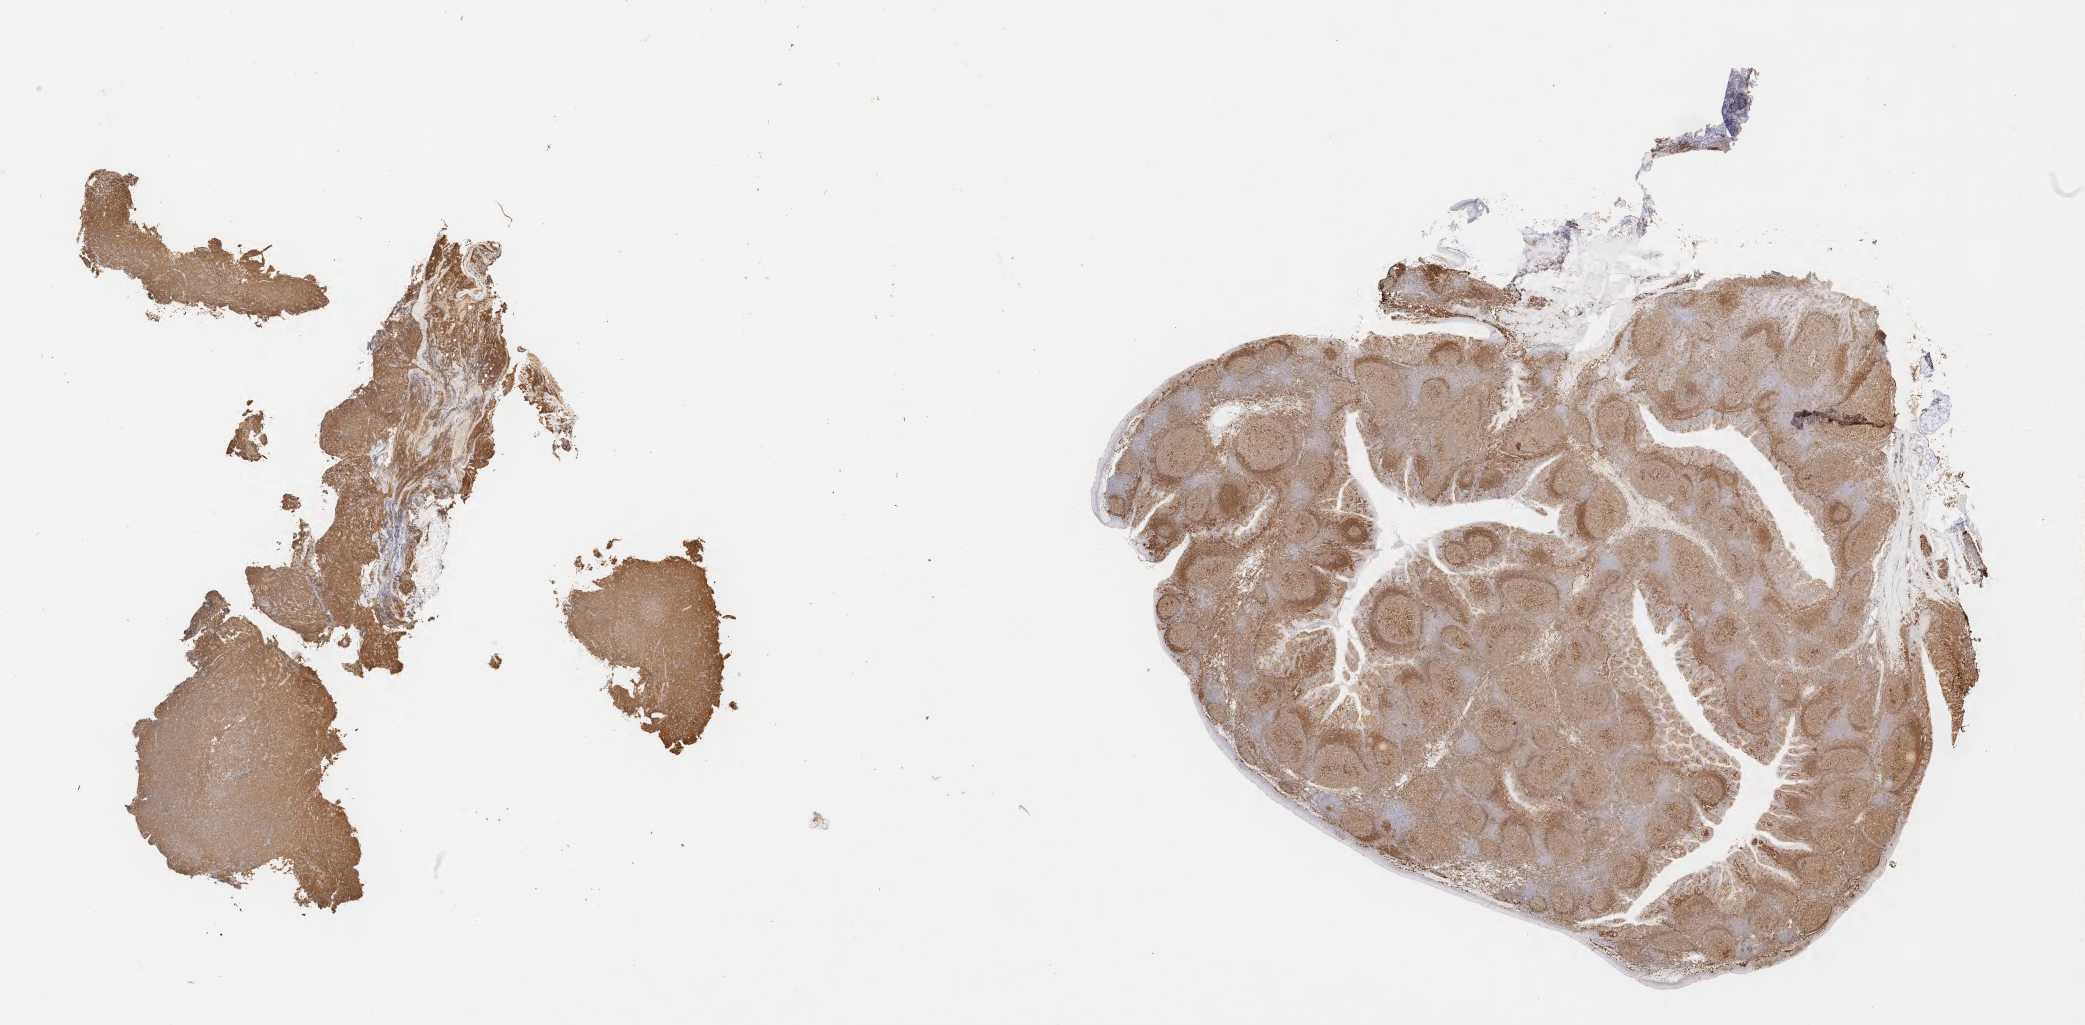
Immunohistochemistry (IHC) whole-slide image stained for CD79a — whole scanned area (about 33.7 x 16.6 mm) shown as a low-resolution overview. Specimen: tumor tissue. Site: liver. Female patient, 36 years old.
Histologic diagnosis: Diffuse large B-cell lymphoma, NOS.